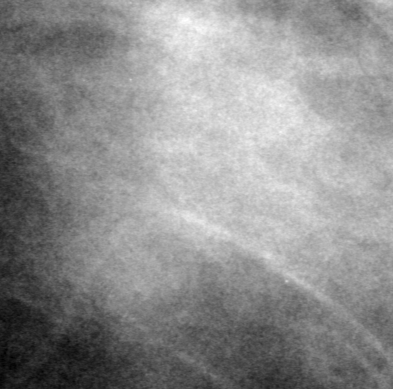
Region of interest cut from a scanned film mammogram (one marked finding), right breast, CC view.
Mass, shape oval, margins obscured; BI-RADS assessment category 0 (incomplete: needs additional imaging); subtlety rating 3 on a 1 (subtle) to 5 (obvious) scale; pathology (as recorded): benign.